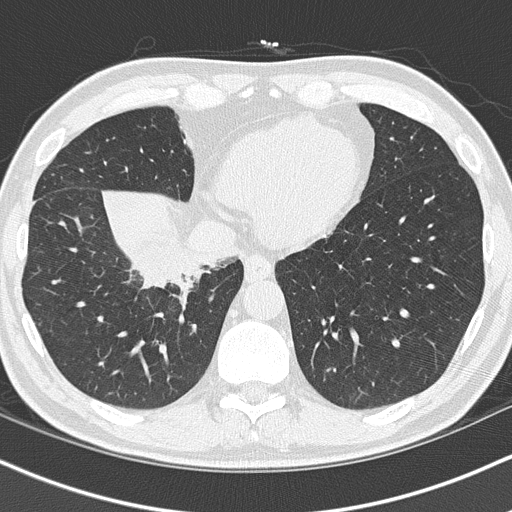
Low-dose screening chest CT, one axial slice; slice 34 of 151 in the series (ordered by position); 120 kVp; lung window (W 1500 / L -600 HU); 2 mm slice thickness; 512 × 512 image matrix.
Structures marked on this image (outlined manually by an expert reader):
- lesion 1 (tumor, hilum of right lung): bounding box (x1, y1, x2, y2) in pixels: (133, 234, 213, 286)